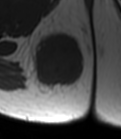
MRI of an extremity soft-tissue mass, one axial slice. Position 21 of 47 along the scan axis. MR volume resampled by the dataset authors to the PET/CT grid (not the native acquisition matrix). 3.27 mm slice thickness. 121 × 139 image matrix, field of view 118 × 136 mm. Female patient. Case-level facts recorded for this patient, not image findings: histological type: epithelioid sarcoma; grade: intermediate; site of the primary tumour: right buttock.
Structures marked on this image (expert contour drawn on MRI and transferred to this co-registered scan by the dataset authors):
- gross tumour volume including surrounding oedema: bounding box (x1, y1, x2, y2) in pixels: (27, 29, 83, 94)
- gross tumour volume (mass): (32, 34, 83, 87)